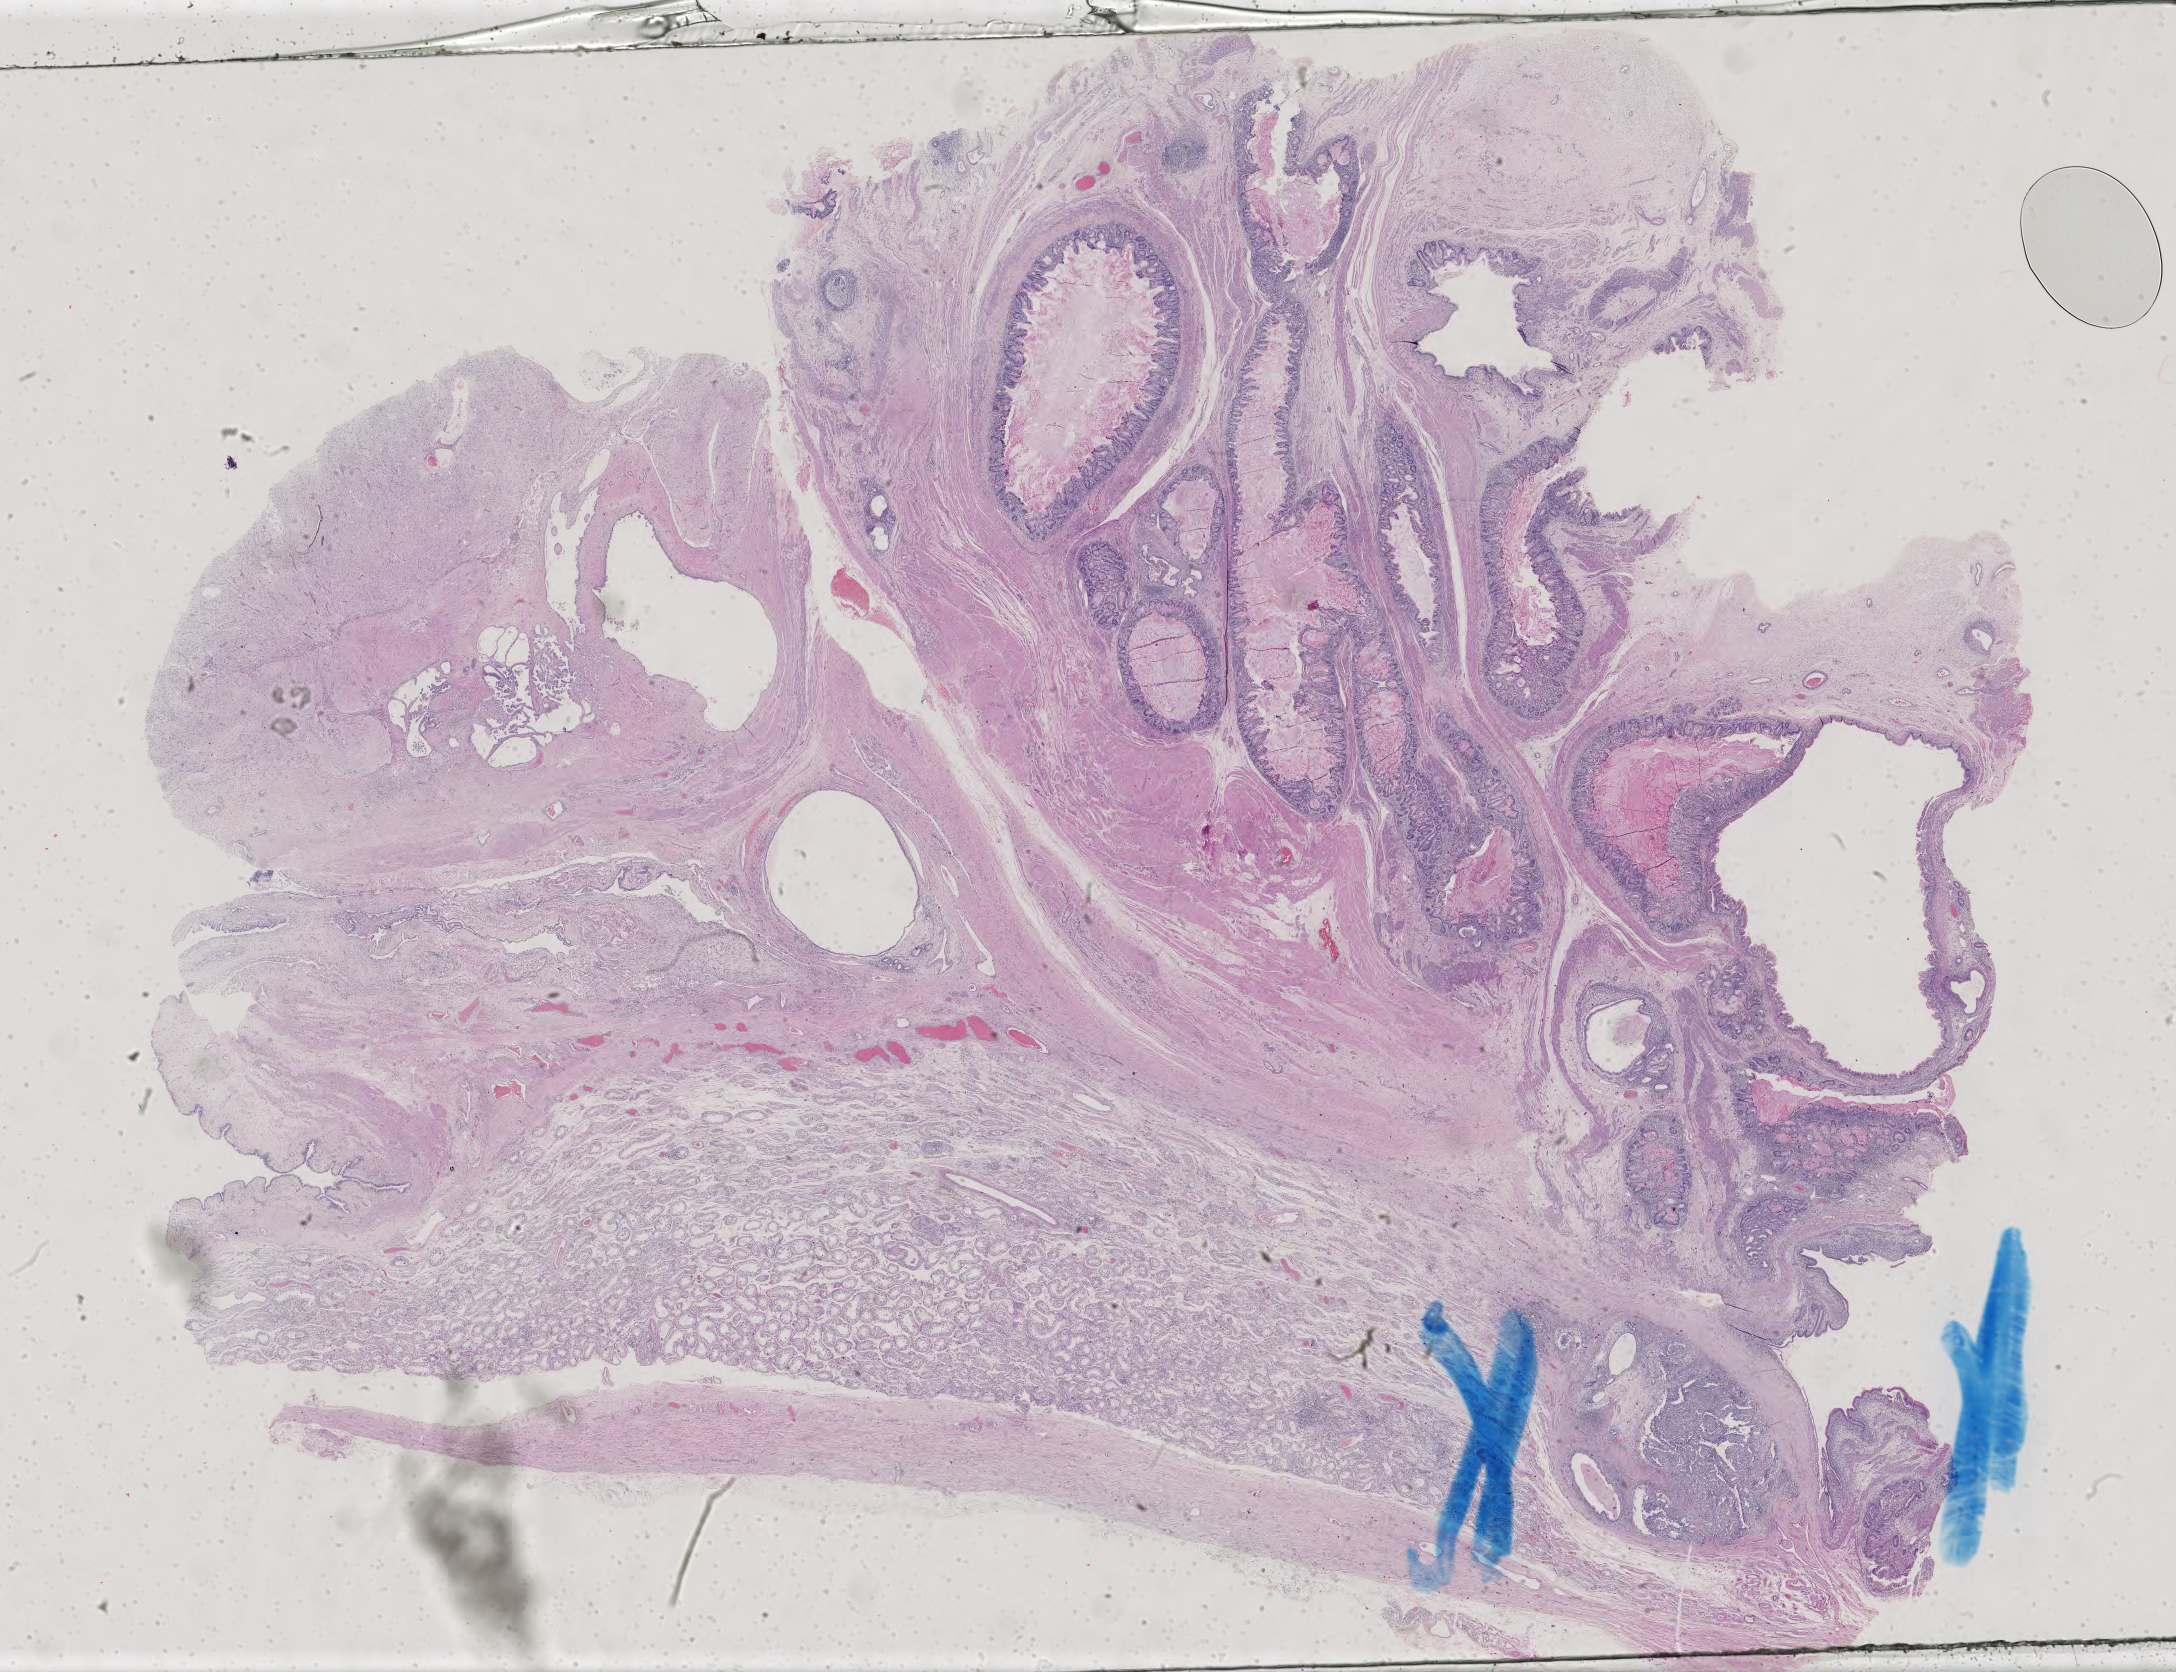
Whole-slide histology image, Hematoxylin and eosin (H&E) stained, a low-resolution overview of the entire scanned area, about 31.7 x 24.4 mm (slide scanned at 40x); formalin-fixed paraffin-embedded (FFPE) diagnostic section; primary tumour sample from the testis. Patient: male, age at initial diagnosis 36 years.
Pathologic diagnosis: Teratoma, benign. AJCC pathologic stage: IS.